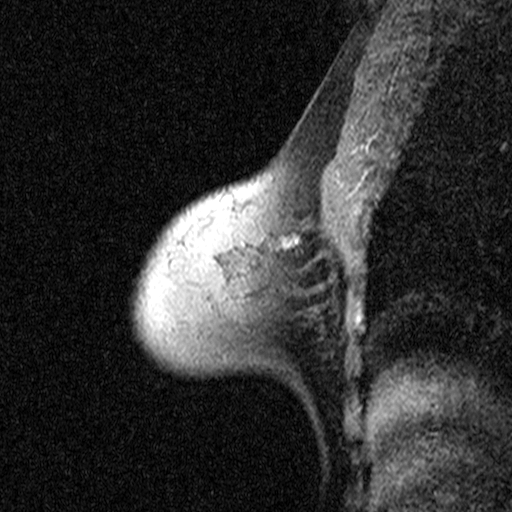
Breast MRI (dynamic contrast-enhanced), one sagittal slice; slice 30 of 44 in the series (ordered by position); dynamic contrast-enhanced study with each time point stored as its own series, time point 2 of 3 at this slice position (early post-contrast, ordered by acquisition time); 1.5 T; TE 4.5 ms, TR 11 ms; 3 mm slice thickness; 512 × 512 image matrix, field of view 200 × 200 mm. Patient: female, 53 years. From the clinical record (not read from this slice): setting: breast cancer imaged before/during neoadjuvant chemotherapy; receptor status: HR-positive, HER2-negative.
Annotated regions visible in this slice (semi-automatic segmentation, software-assisted and operator-edited):
- analysis volume of interest (the breast-tissue region the enhancement analysis was run in; not a lesion): bounding box <186,216,307,311> (left, top, right, bottom; pixels)
- tumour enhancement mask (voxels above the 90 % enhancement threshold inside the analysis volume of interest): <283,243,292,245>